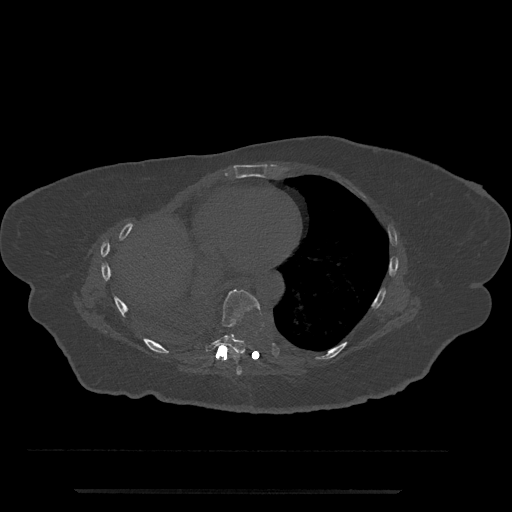
CT including the spine, one axial slice; position 388 of 797 along the scan axis; reconstruction kernel Br40s/3; 120 kVp; bone window (W 1800 / L 400 HU); 0.5 mm slice thickness; 512 × 512 image matrix, field of view 440 × 440 mm. Patient: female, 51 years. Case-level facts recorded for this patient, not image findings: primary cancer: neuro; vertebrae with lytic lesions (as recorded): T8.
Outlined on this slice (semi-automatically segmented with operator editing):
- T7 vertebra: bounding box [x1, y1, x2, y2] px = [236, 365, 242, 375]
- T8 vertebra: [204, 289, 261, 354]
- T9 vertebra: [231, 334, 234, 337]